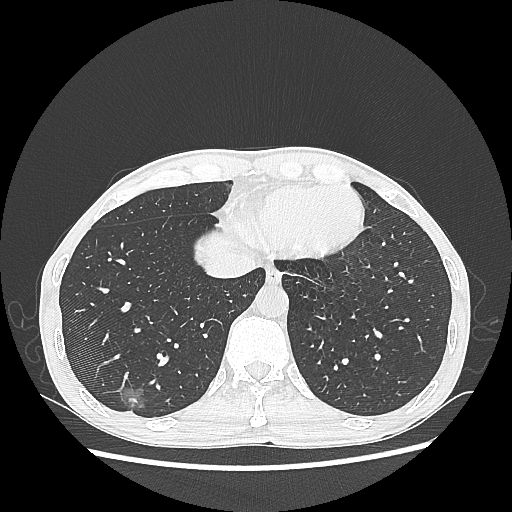
Chest CT, one axial slice. Position 71 of 270 along the scan axis. Reconstruction kernel LUNG. 100 kVp. Lung window (W 1500 / L -600 HU). 512 × 512 image matrix, field of view 360 × 360 mm. Patient: male, 60 years. From the clinical record (not read from this slice): clinical TNM (as recorded): T1c N0 M0; histopathological grade: G2.
Structures marked on this image (bounding box drawn by a radiologist):
- lung tumour (recorded histology: adenocarcinoma): bounding box (x1, y1, x2, y2) in pixels: (119, 375, 154, 424)